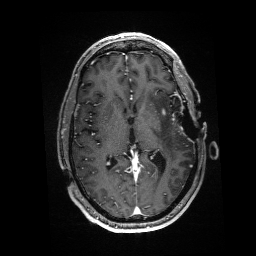
Brain MRI from a brain-tumour surgery series, one axial slice. Position 84 of 176 along the scan axis. T1-weighted post-contrast. 1 mm slice thickness. 256 × 256 image matrix, field of view 256 × 256 mm. From the clinical record (not read from this slice): histopathology: Glioblastoma; WHO grade: 4; IDH mutation: no.
Outlined on this slice (expert manual segmentation):
- residual tumour: box from (x=161, y=110) to (x=166, y=115) px